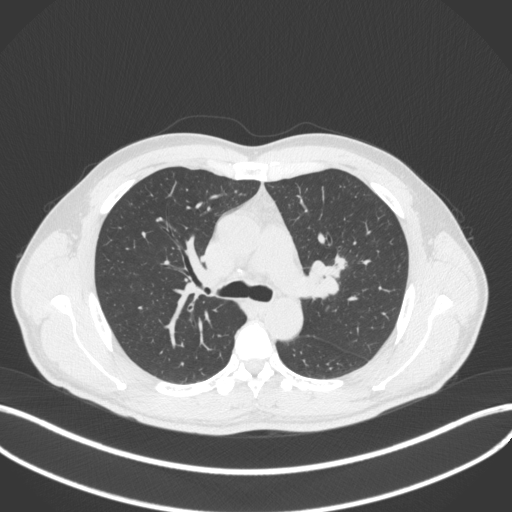
Chest CT, one axial slice; position 276 of 383 along the scan axis; reconstruction kernel B31f; lung window (W 1500 / L -600 HU); 1 mm slice thickness; 512 × 512 image matrix. Male patient, age 50 years. From the clinical record (not read from this slice): clinical TNM (as recorded): T1c N1 M1b.
Annotated regions visible in this slice (rectangle marked by the reading radiologist):
- lung tumour (recorded histology: squamous cell carcinoma): bounding box [x1, y1, x2, y2] px = [307, 246, 348, 305]